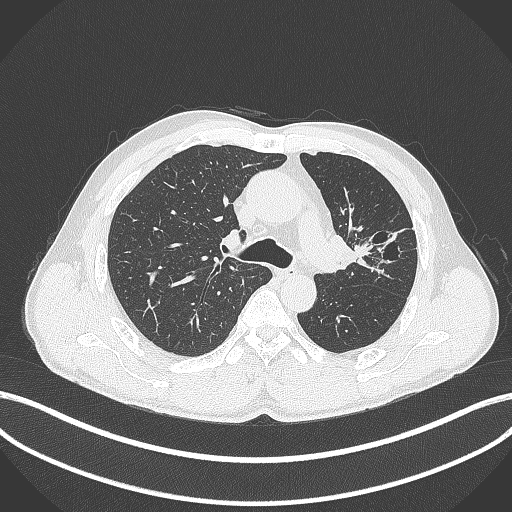
Chest CT, one axial slice; position 277 of 429 along the scan axis; reconstruction kernel B70f; 120 kVp; lung window (W 1500 / L -600 HU); 1 mm slice thickness; 512 × 512 image matrix. Male patient, age 57 years. Case-level facts recorded for this patient, not image findings: clinical TNM (as recorded): T2b N0 M0.
Annotated regions visible in this slice (rectangle marked by the reading radiologist):
- lung tumour (recorded histology: squamous cell carcinoma): bounding box [x1, y1, x2, y2] px = [333, 230, 393, 280]